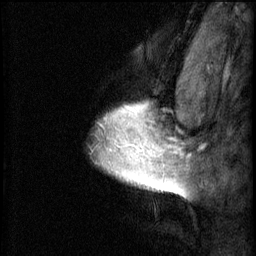
Breast MRI (dynamic contrast-enhanced), one sagittal slice; position 53 of 60 along the scan axis; 3 images stored at this slice position (order not interpretable as contrast timing); 1.5 T; TE 4.2 ms, TR 8.2 ms; 256 × 256 image matrix, field of view 180 × 180 mm. Female patient, age 40 years.
Outlined on this slice (semi-automatically segmented with operator editing):
- analysis volume of interest (the breast-tissue region the enhancement analysis was run in; not a lesion): box from (x=96, y=100) to (x=167, y=193) px
- tumour enhancement mask (voxels above the 70 % enhancement threshold inside the analysis volume of interest): (x=100, y=104)–(x=167, y=191)